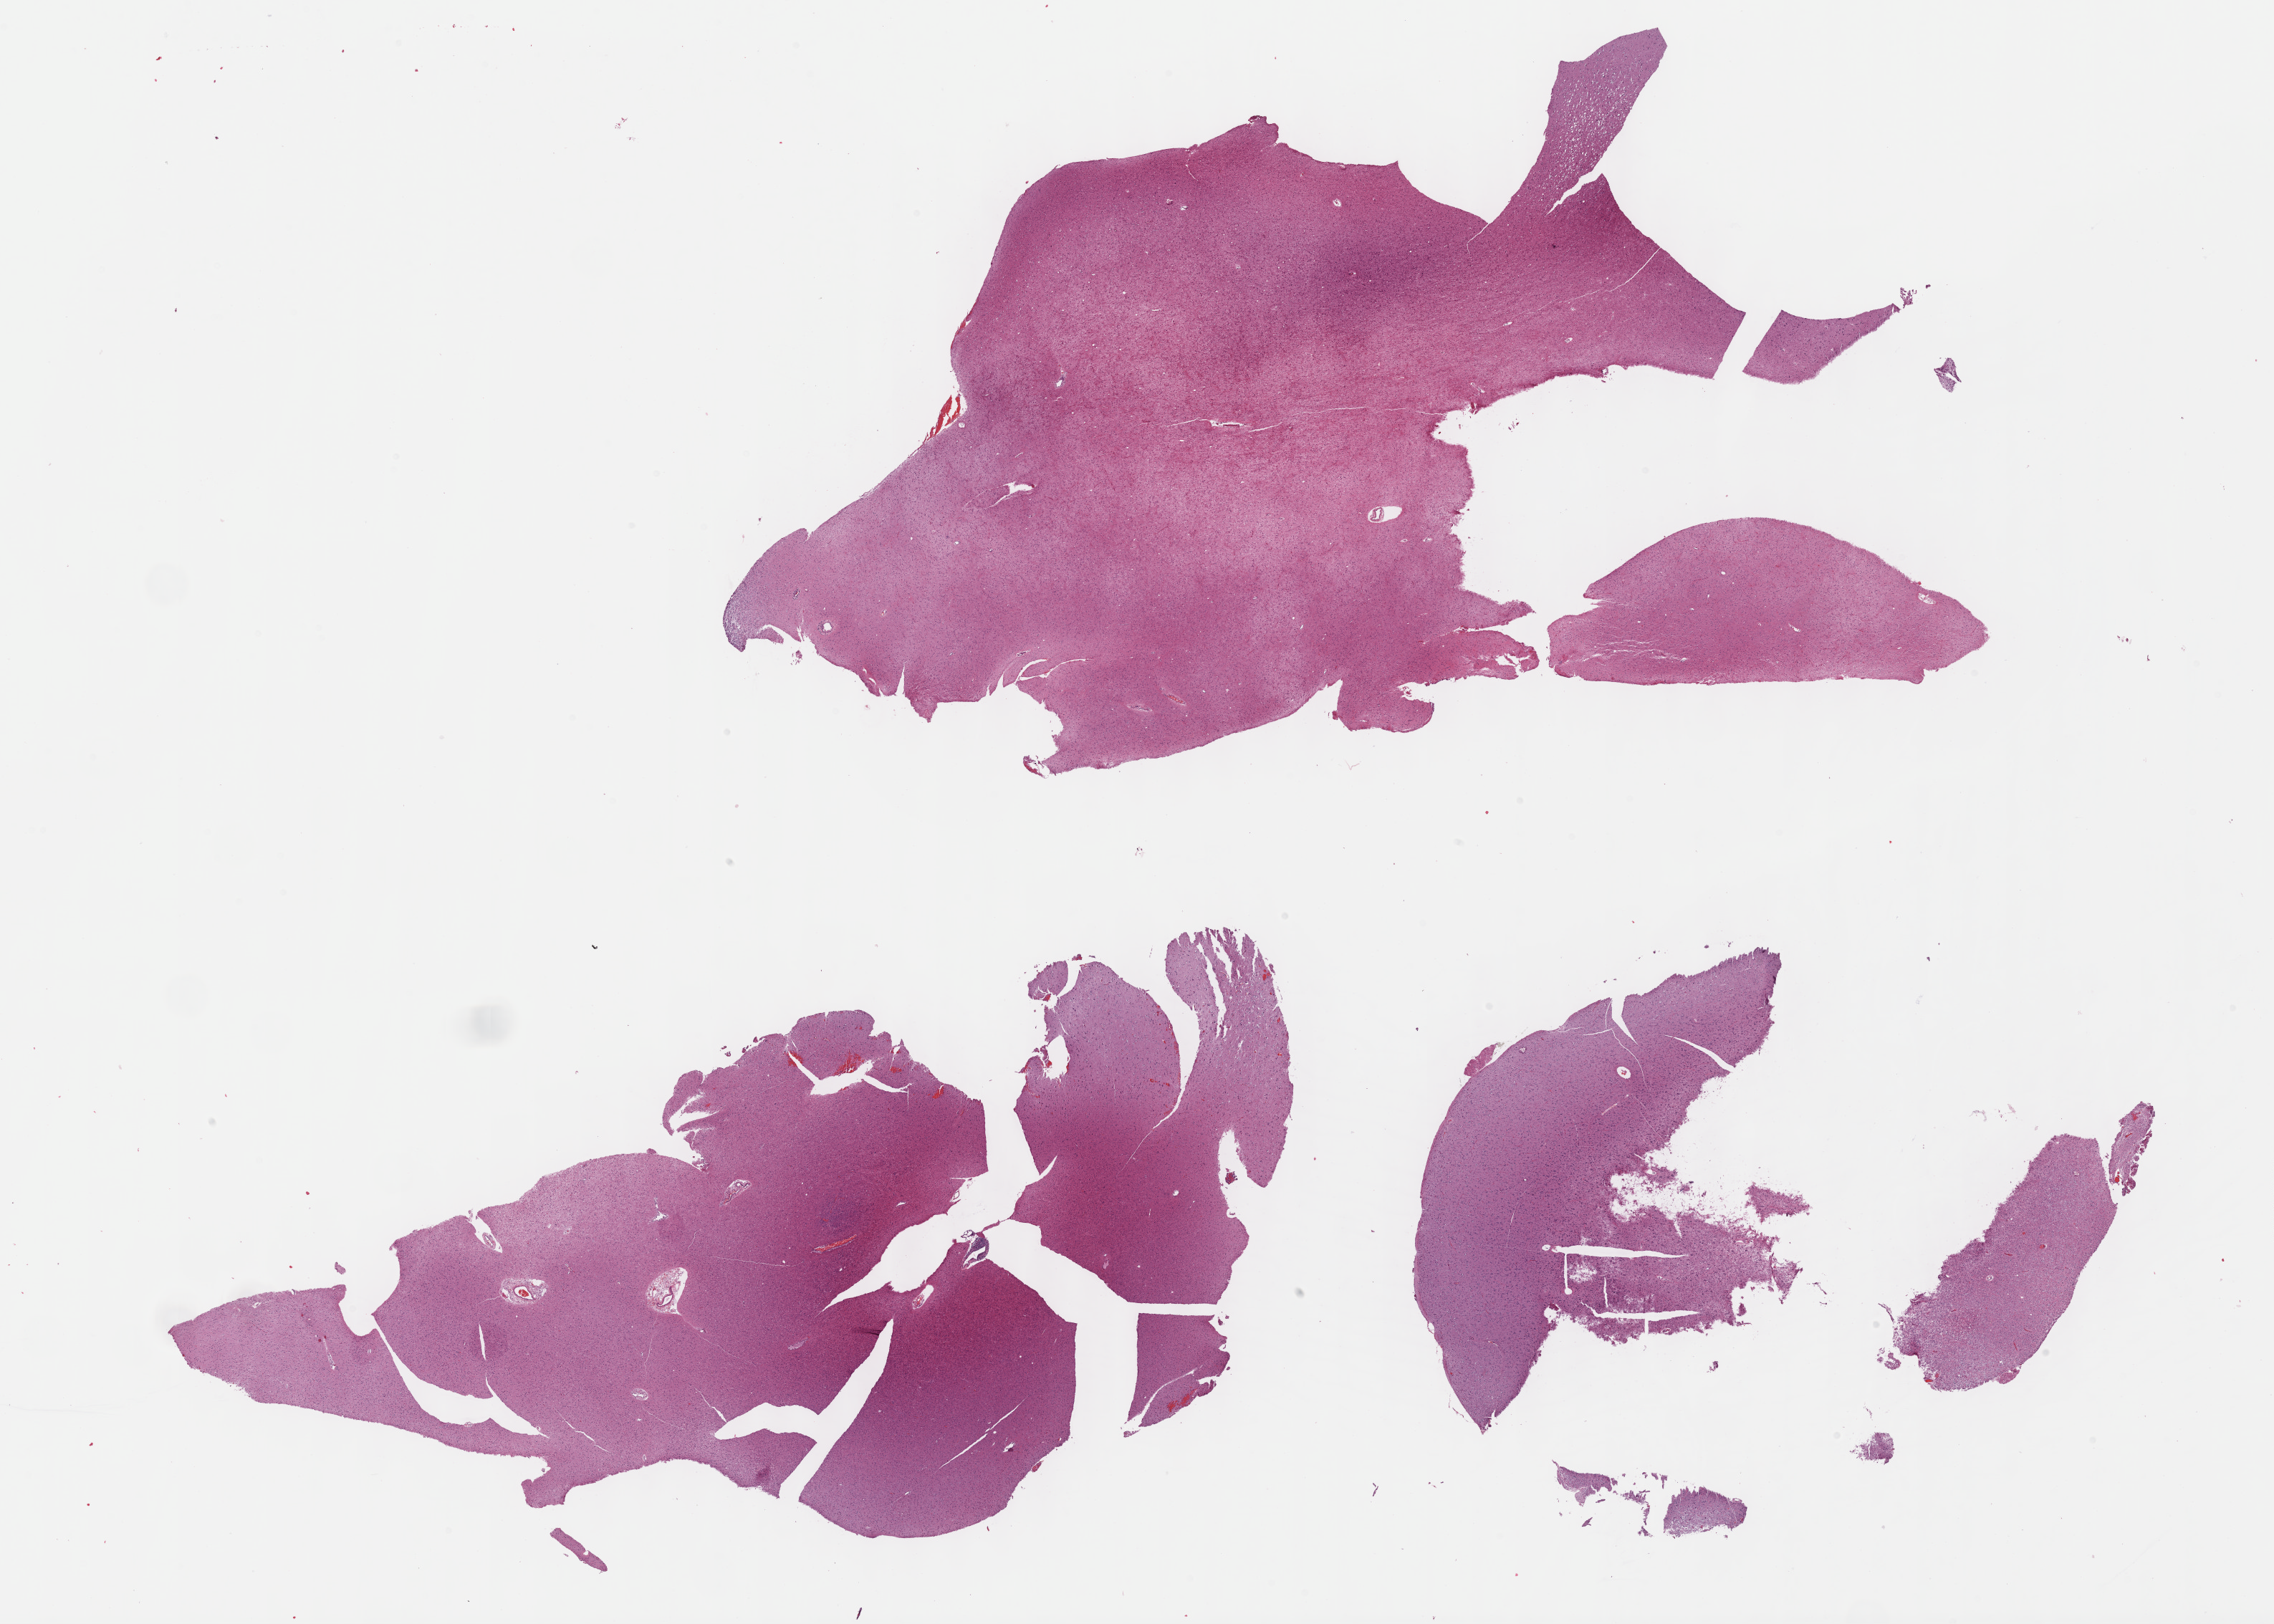
Hematoxylin and eosin (H&E) stained whole-slide image — shown as a low-resolution overview of the whole scanned area (about 25.7 x 18.3 mm, slide scanned at 40x), FFPE section, sample: primary tumour, brain. Patient: male, age at initial diagnosis 38 years.
Pathologic diagnosis: Oligodendroglioma, NOS.